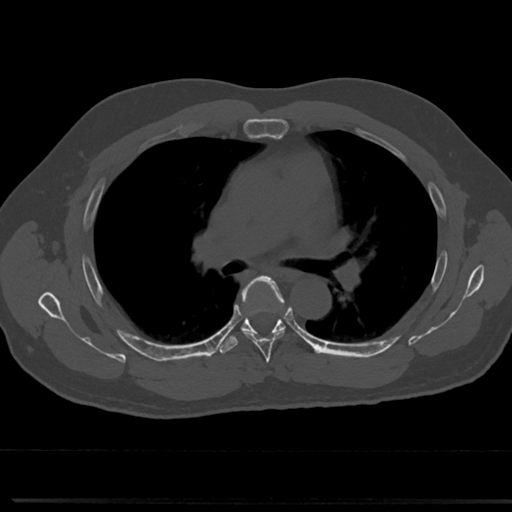
CT including the spine, one axial slice; position 480 of 817 along the scan axis; bone window (W 1800 / L 400 HU); 512 × 512 image matrix, field of view 355 × 355 mm. Male patient, age 61 years. Case-level facts recorded for this patient, not image findings: primary cancer: prostate.
Outlined on this slice (semi-automatic segmentation, software-assisted and operator-edited):
- T5 vertebra: bounding box (x1, y1, x2, y2) in pixels: (238, 277, 288, 358)
- T6 vertebra: (241, 325, 286, 334)